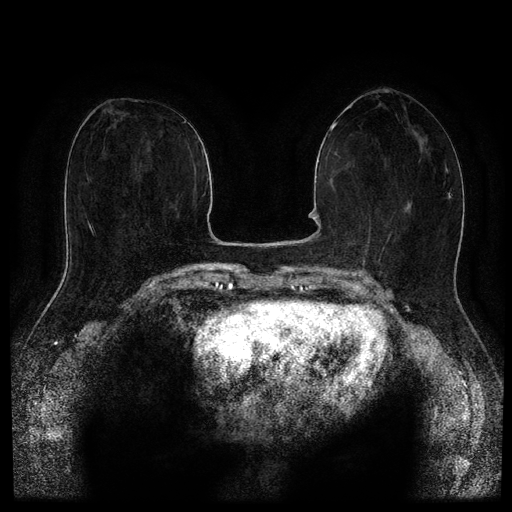
Breast MRI (dynamic contrast-enhanced, multi-phase), one axial slice; slice 52 of 116 in the series (ordered by position); dynamic contrast-enhanced series, time point 2 of 5 at this slice position (early post-contrast); 1.5 T; TE 2.6 ms, TR 5.3 ms; 2.1 mm slice thickness; 512 × 512 image matrix, field of view 350 × 350 mm. Female patient, age 66 years.
Outlined on this slice (semi-automatically segmented with operator editing):
- breast lesion (labelled benign in the annotation): bounding box <404,203,411,213> (left, top, right, bottom; pixels)